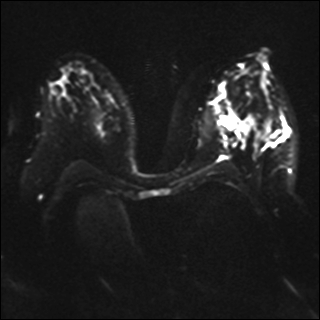
Breast MRI, one axial slice; diffusion-weighted series; image 2 of 4 stored at this slice position (different b-values; order by instance number); 1.5 T; 4 mm slice thickness; 320 × 320 image matrix. Female patient.
Structures marked on this image (outlined manually by an expert reader):
- tumour on diffusion-weighted imaging: box from (x=226, y=114) to (x=249, y=138) px